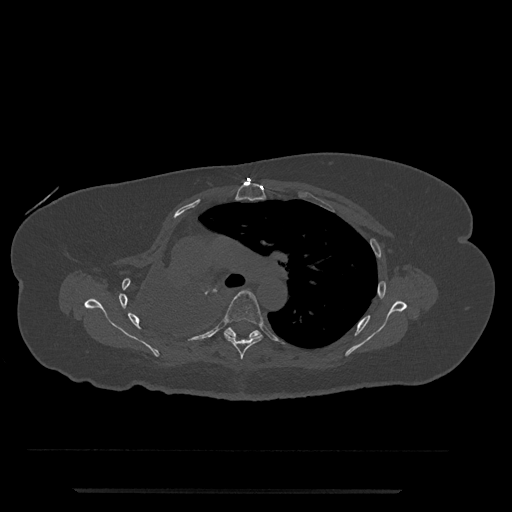
CT including the spine, one axial slice. 120 kVp. Bone window (W 1800 / L 400 HU). 512 × 512 image matrix, field of view 440 × 440 mm. Patient: female, 51 years. From the clinical record (not read from this slice): primary cancer: neuro; vertebrae with lytic lesions (as recorded): T8.
Annotated regions visible in this slice (semi-automatically segmented with operator editing):
- T5 vertebra: bounding box <224,290,264,359> (left, top, right, bottom; pixels)
- T6 vertebra: <224,327,261,339>